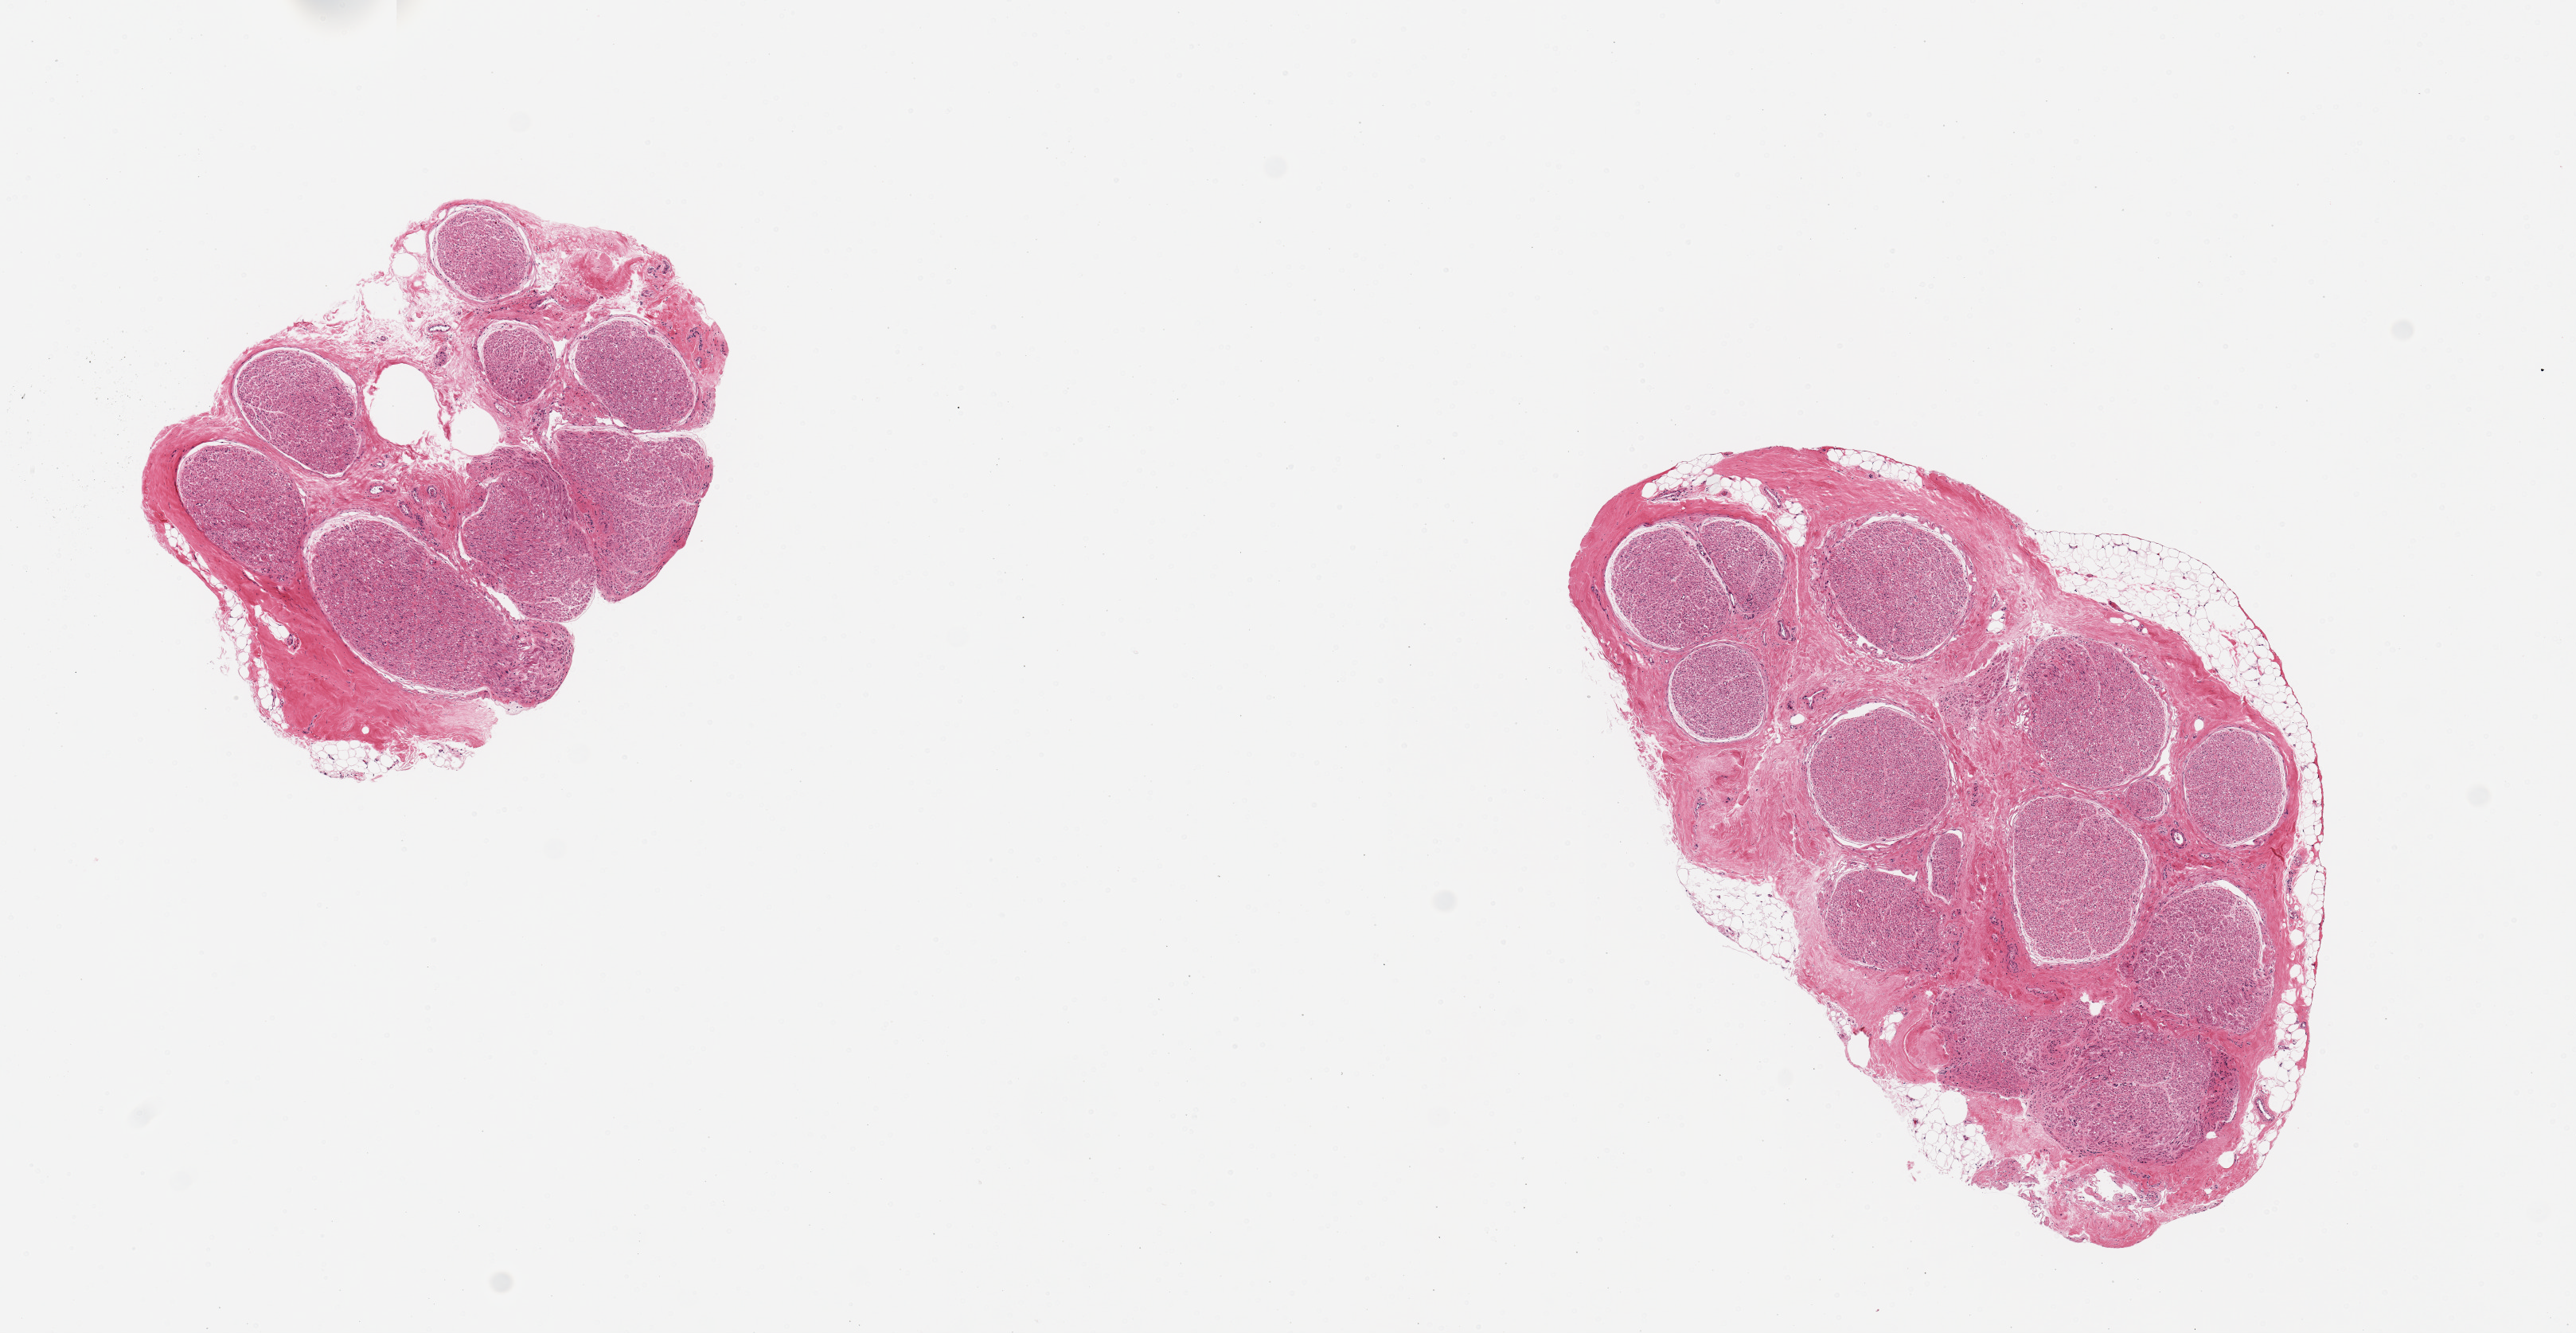
Whole-slide image, hematoxylin and eosin (H&E) stain, brightfield, shown as a low-resolution overview of the whole scanned area (about 12.8 x 6.6 mm, acquisition: 20x scan); PAXgene-fixed paraffin-embedded (PFPE) section; target tissue: tibial nerve; tissue donor sample. Donor sex: female.
- reviewer comment on this tissue sample: 2 pieces; small amounts of external/internal fat and connective tissue